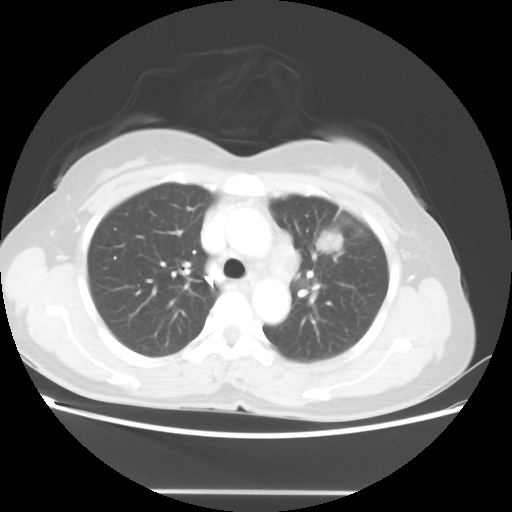
Chest CT, one axial slice. Position 32 of 46 along the scan axis. 100 kVp. Lung window (W 1500 / L -600 HU). 512 × 512 image matrix. Female patient, age 50 years. Case-level facts recorded for this patient, not image findings: clinical TNM (as recorded): T1c N1 M0.
Annotated regions visible in this slice (rectangle marked by the reading radiologist):
- lung tumour (recorded histology: adenocarcinoma): bounding box <320,233,343,250> (left, top, right, bottom; pixels)